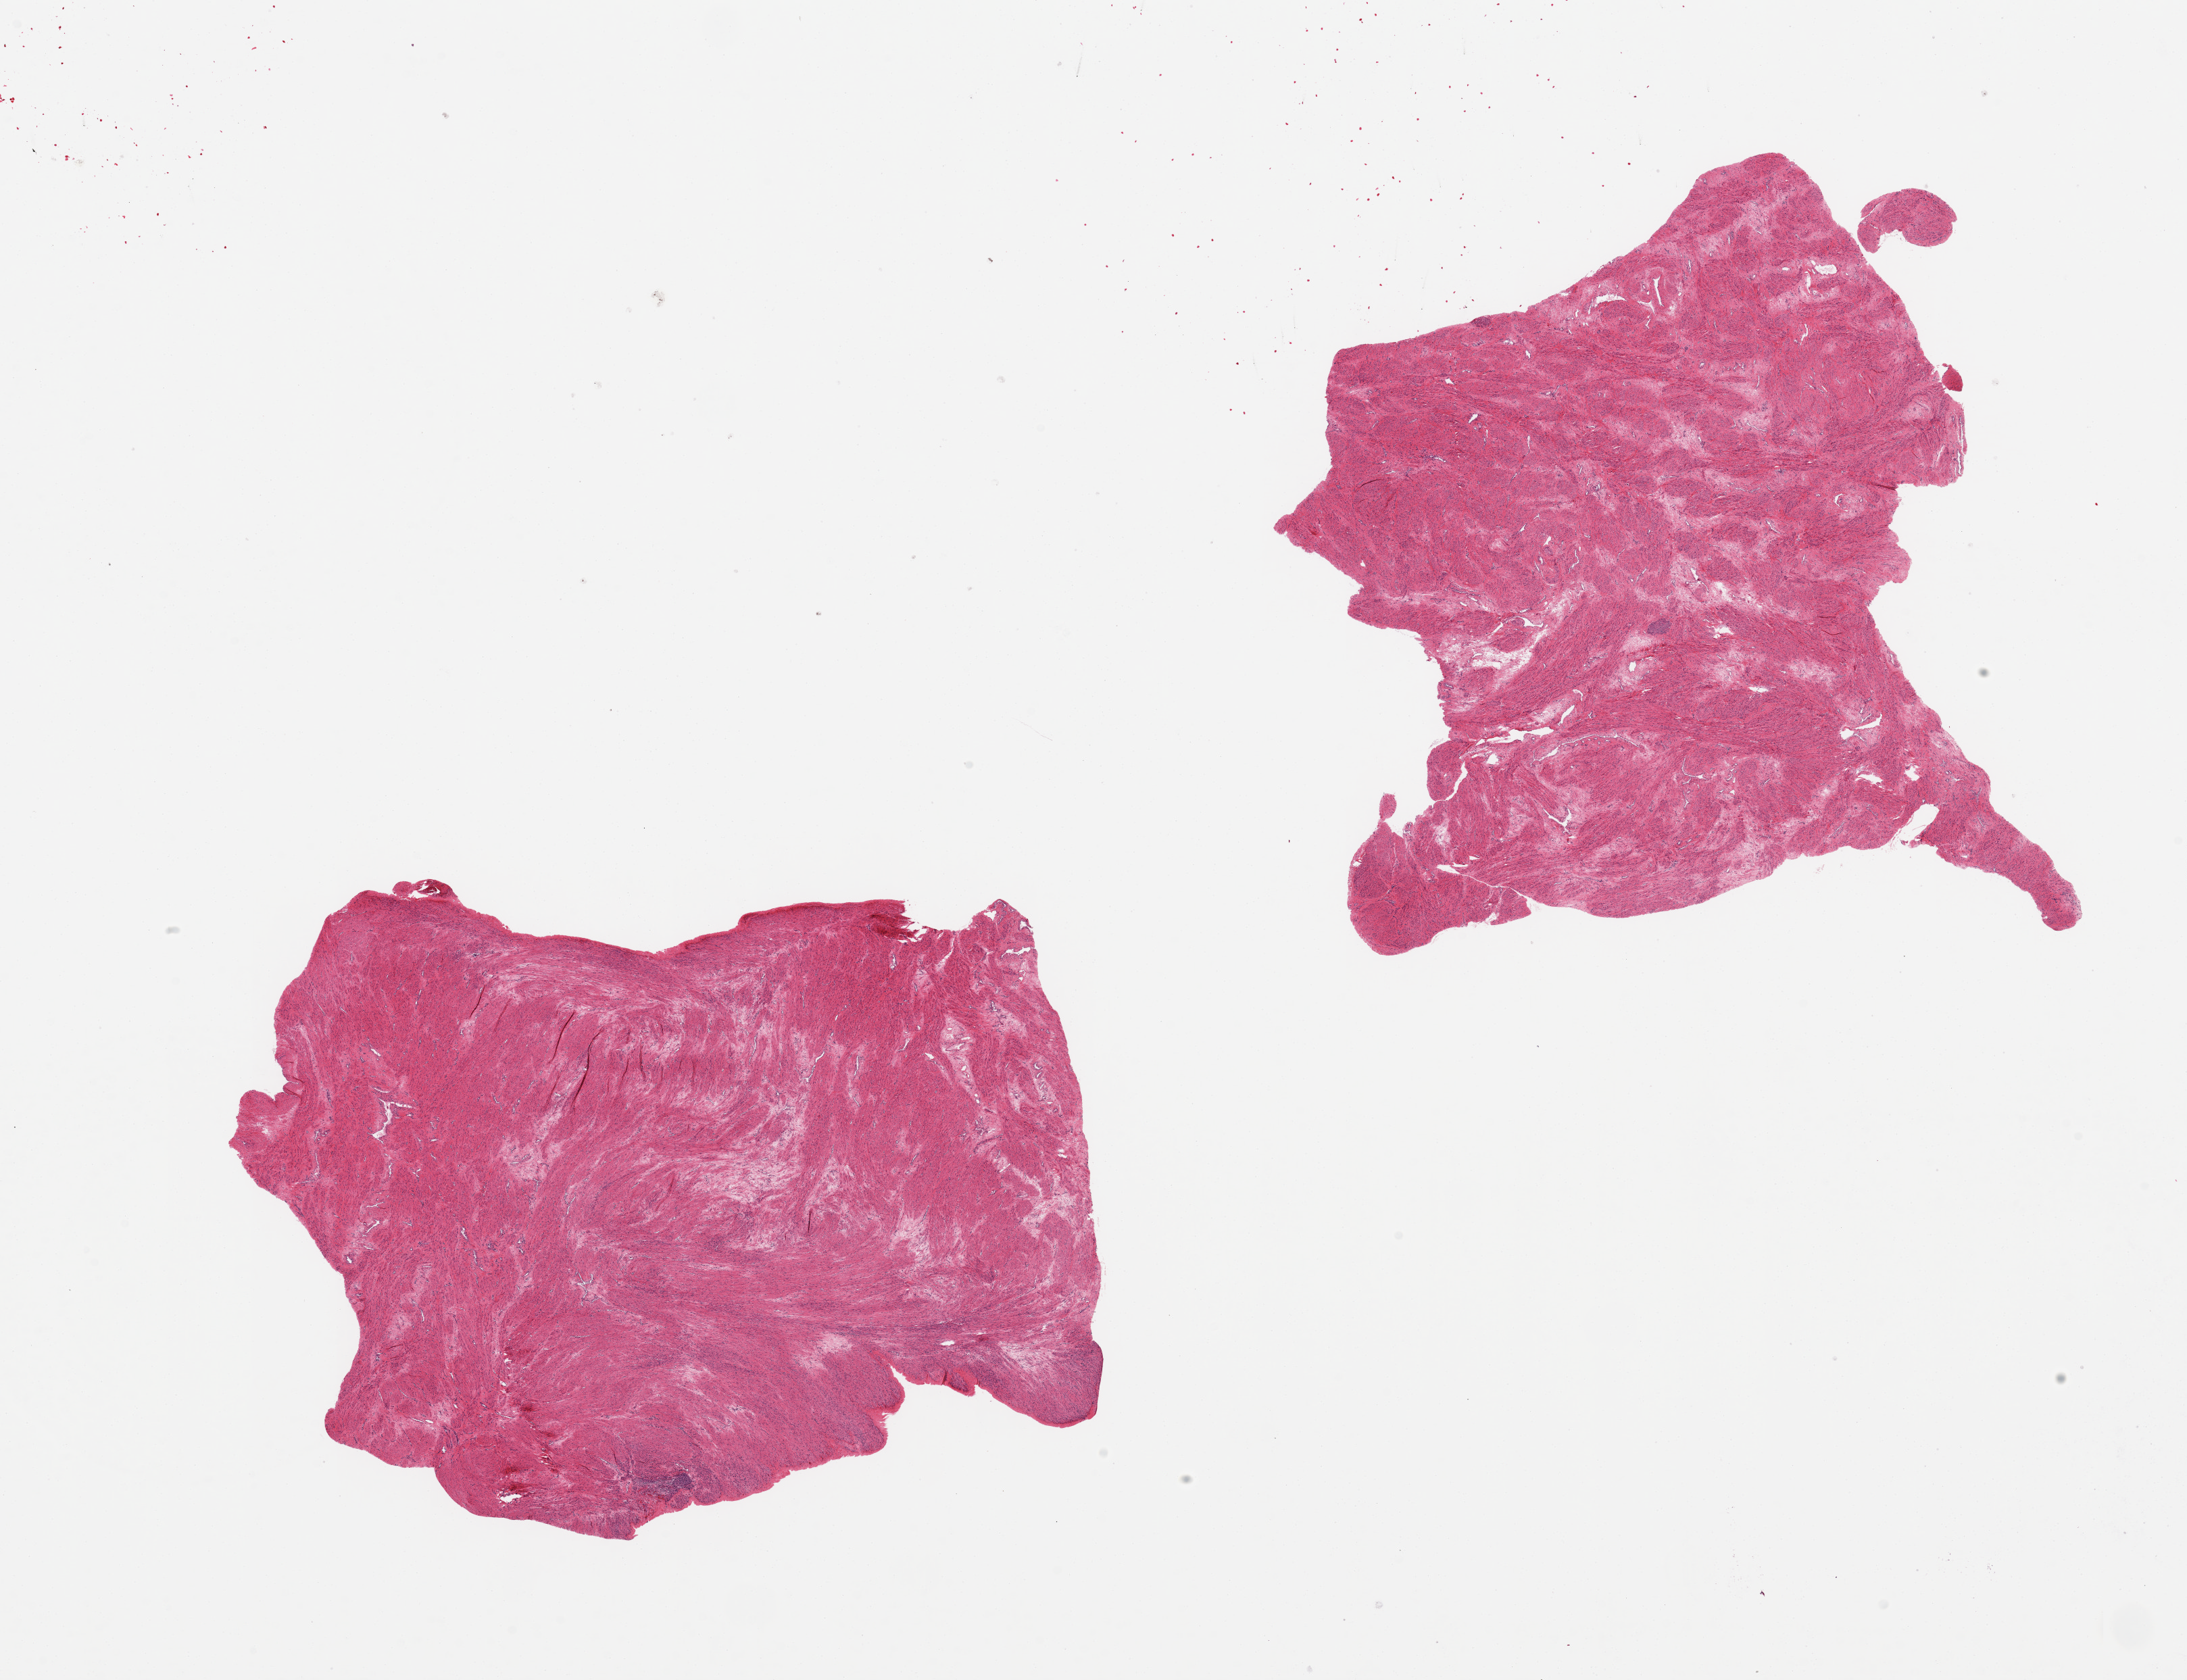
Whole-slide image, haematoxylin and eosin stain, low-resolution overview of the scanned area, about 25.6 x 19.7 mm; PAXgene-fixed paraffin-embedded (PFPE) section; target tissue: uterus; tissue donor sample. Donor sex: female.
- pathologist's review note for this sample: 2 aliquots, ~ 9x7mm. All myometrium, no visible endometrial glands or stroma